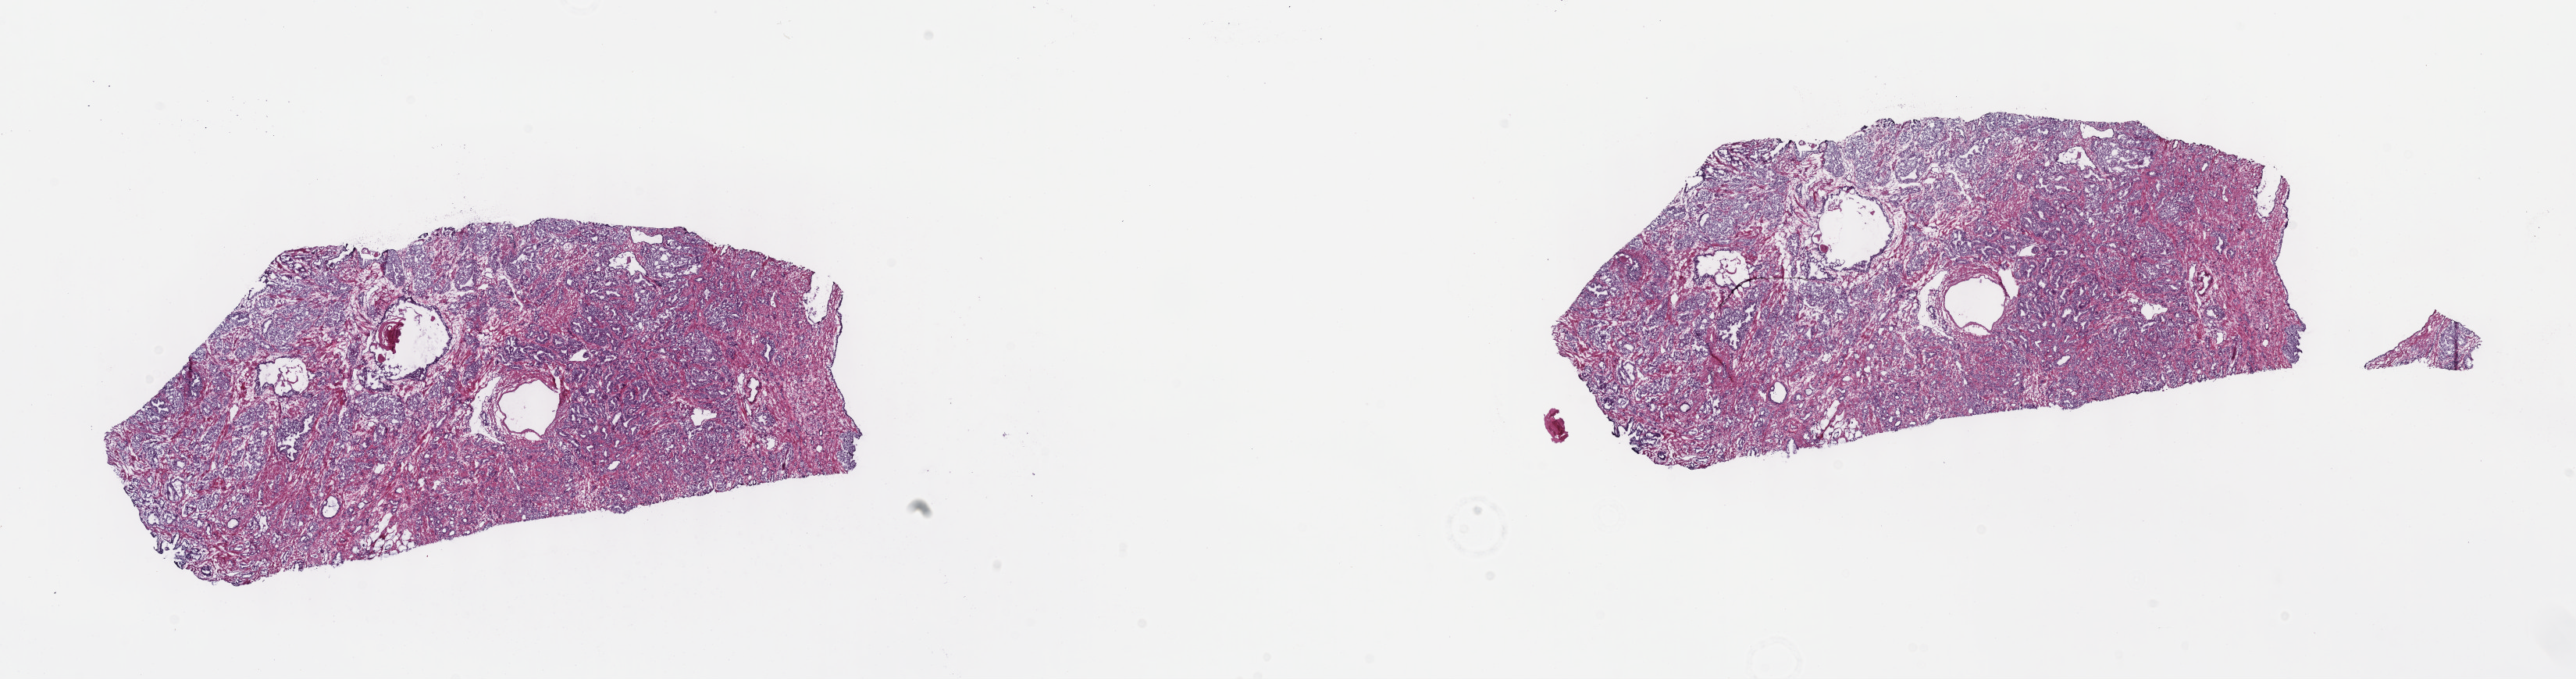
Digitized Hematoxylin and eosin (H&E) stained tissue section (whole slide), low-resolution overview of the scanned area, about 26.7 x 7.0 mm, frozen section from the top of the tissue portion, prostate, primary tumour sample. Male, age 59 years at initial diagnosis. Gleason score: 7 (4+3). Slide review estimates, as recorded: tumour cells 50%, tumour nuclei 90%, normal cells 2%, stromal cells 48%, necrosis 0%. Infiltration values recorded for this section: lymphocyte infiltration 3%, monocyte infiltration 1%, neutrophil infiltration 1%.
Laterality: bilateral. Diagnosis: Adenocarcinoma, NOS.